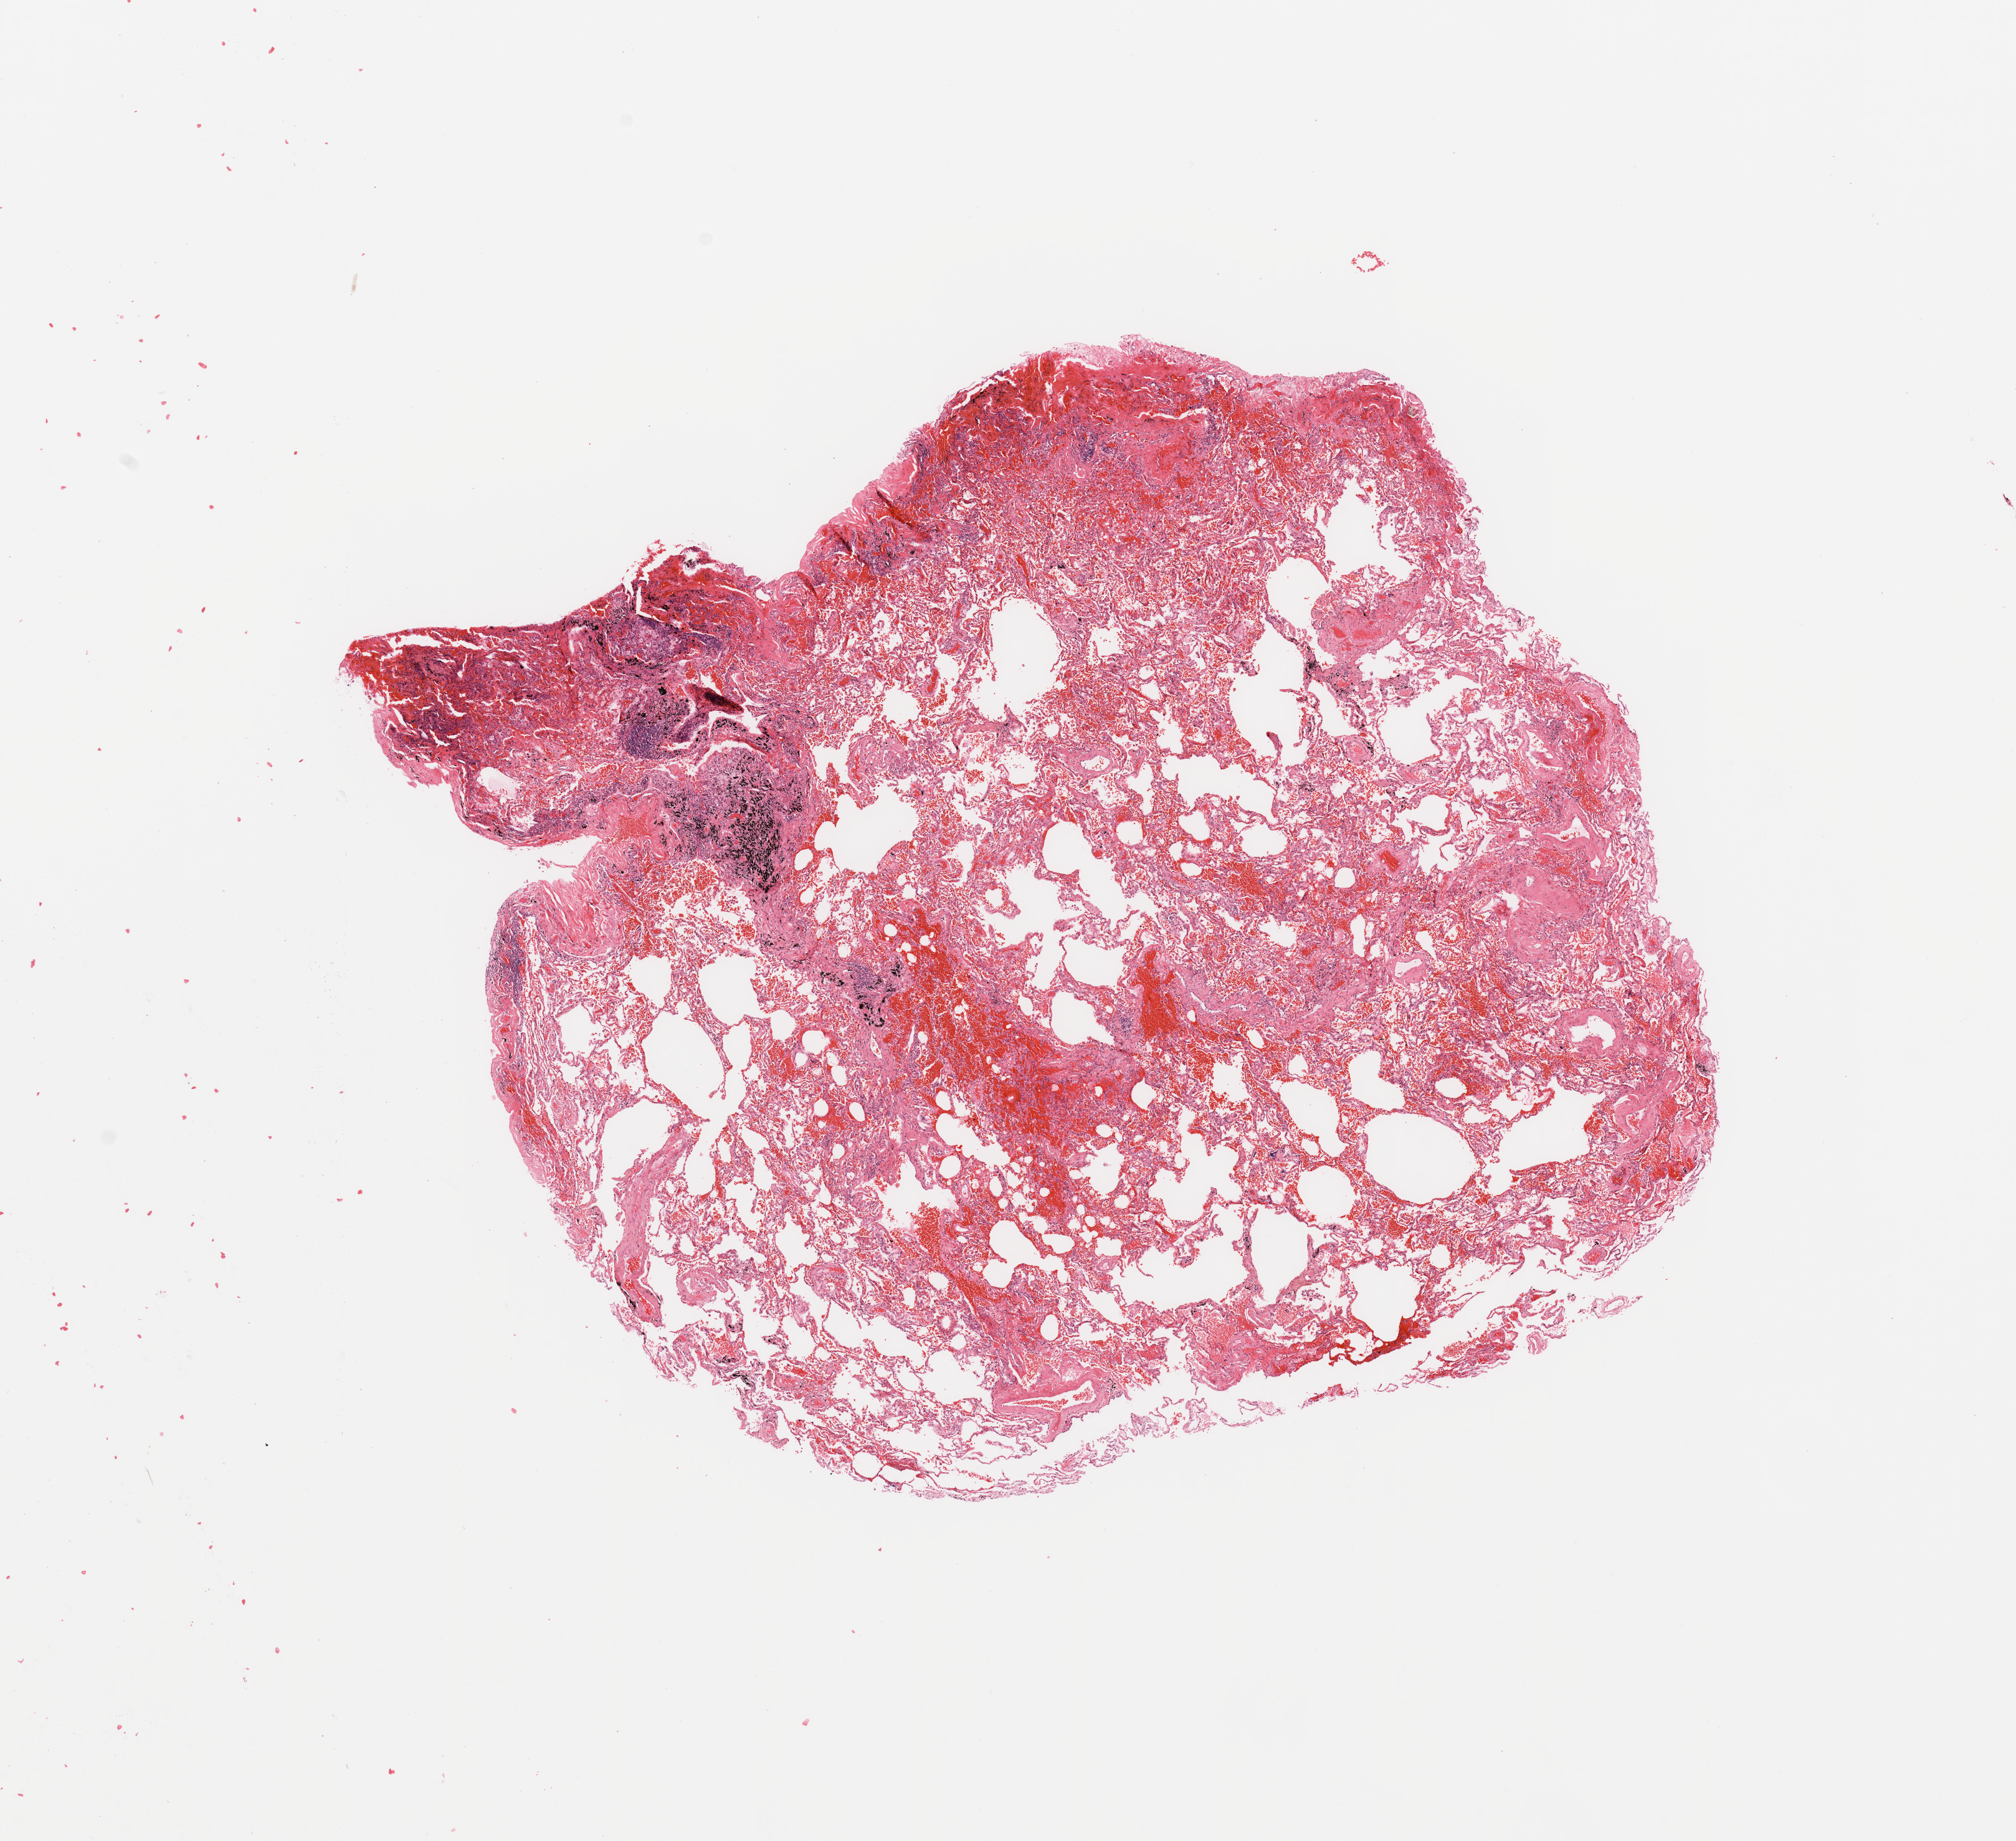
Whole-slide histology image, H&E — low-resolution overview of the scanned area, about 12.8 x 11.7 mm. Normal (non-tumour) tissue sample, sampled site: lung. Patient: male, age 72 years.
This section: normal (non-tumour) tissue from the same patient. Patient diagnosis: Adenocarcinoma, NOS.